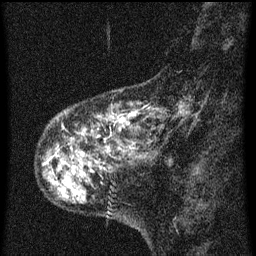
Breast MRI (dynamic contrast-enhanced), one sagittal slice. Slice 12 of 60 in the series (ordered by position). Dynamic contrast-enhanced series, image 2 of 3 at this slice position (ordered by acquisition). 1.5 T. TE 4.2 ms, TR 8 ms. 2 mm slice thickness. 256 × 256 image matrix, field of view 180 × 180 mm. Patient: female, 55 years.
Outlined on this slice (semi-automatic segmentation, software-assisted and operator-edited):
- analysis volume of interest (the breast-tissue region the enhancement analysis was run in; not a lesion): bounding box (x1, y1, x2, y2) in pixels: (40, 92, 177, 159)
- tumour enhancement mask (voxels above the 70 % enhancement threshold inside the analysis volume of interest): (50, 110, 137, 159)